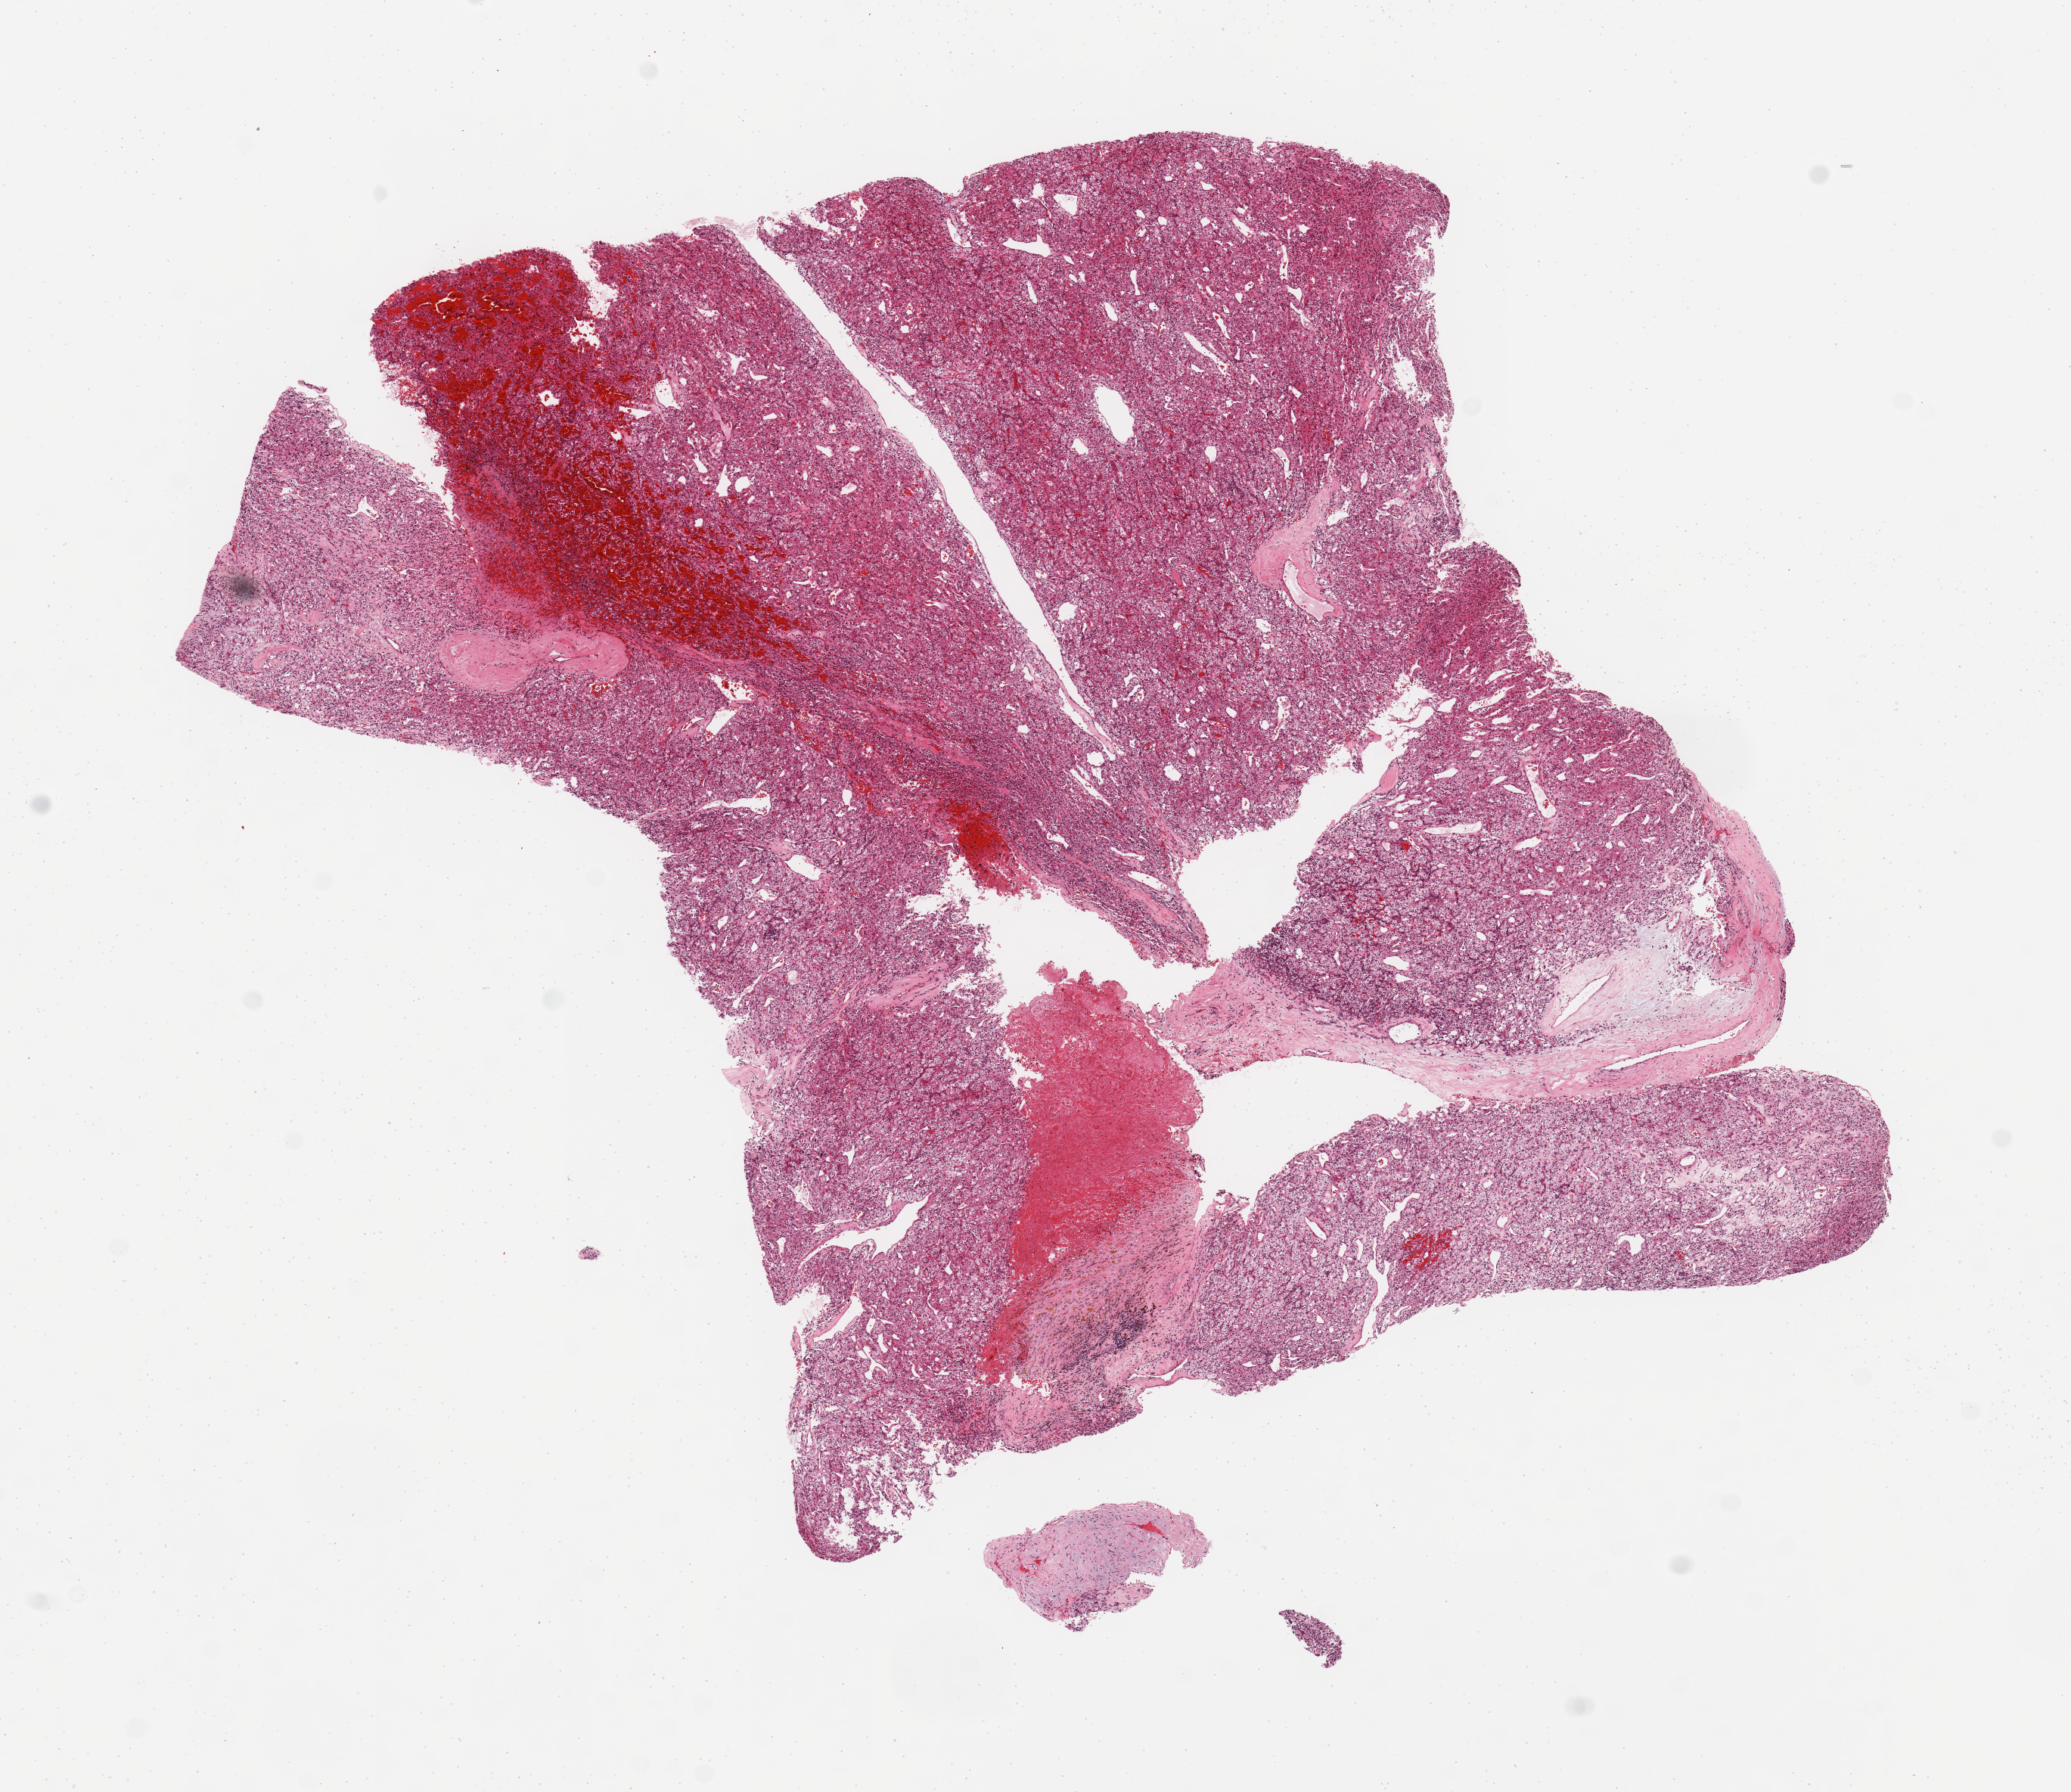
Digitized H&E-stained tissue section (whole slide), whole scanned area (about 10.8 x 9.4 mm, slide scanned at 20x) shown as a low-resolution overview; tumour tissue sample, sampled site: kidney. Female, 75 y/o. Histologic grade: G3 (poorly differentiated). Composition of this section per pathologist review: tumour nuclei 90%, necrosis 5%.
AJCC pathologic stage: III. Histologic diagnosis: Renal cell carcinoma, NOS.